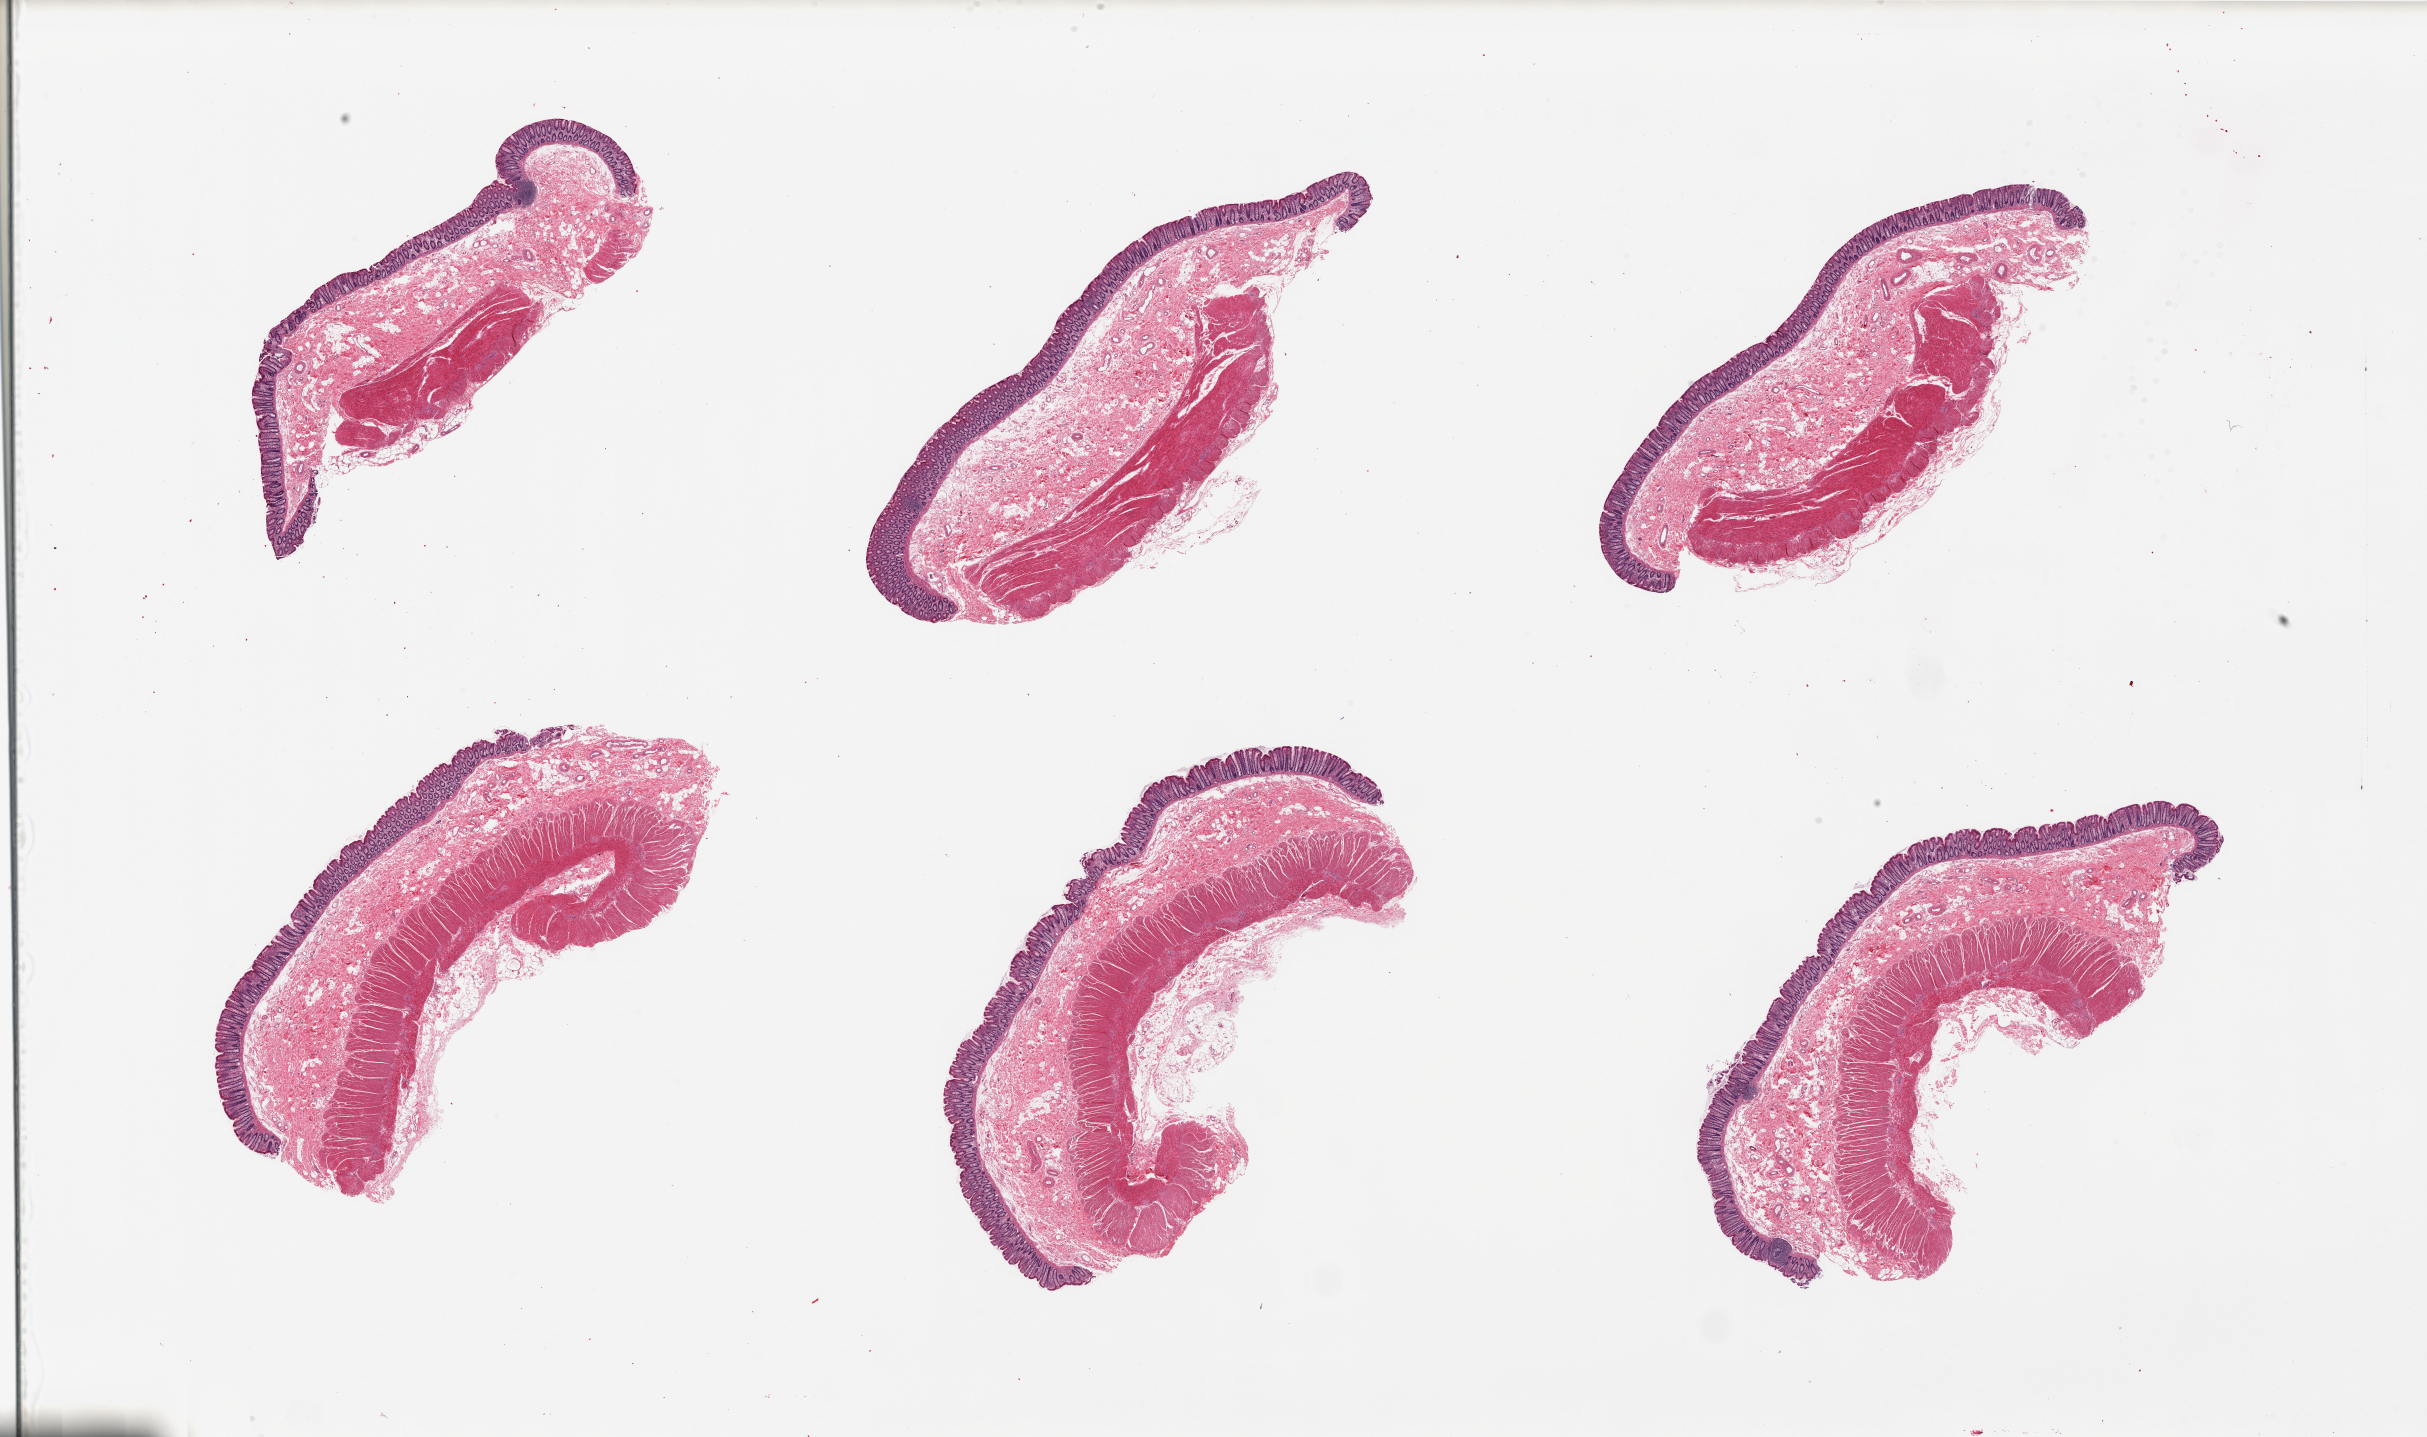
Whole-slide image, haematoxylin and eosin stain — low-resolution overview of the scanned area, about 38.4 x 22.7 mm; PAXgene-fixed, paraffin-embedded tissue; section of transverse colon (target tissue); donor tissue sample.
Review note (as recorded): 6 pieces. Well dissected full thickness wall.